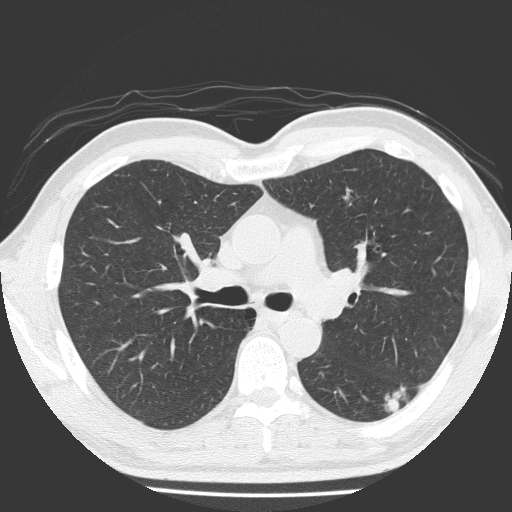
Low-dose screening chest CT, one axial slice. Slice 114 of 184 in the series (ordered by position). Lung window (W 1500 / L -600 HU). 2 mm slice thickness. 512 × 512 image matrix, field of view 348 × 348 mm.
Structures marked on this image (outlined manually by an expert reader):
- lesion 1 (tumor, lower lobe of left lung): bounding box [x1, y1, x2, y2] px = [384, 385, 406, 412]